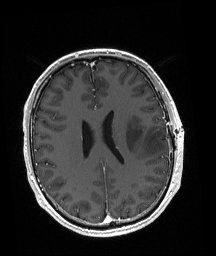
Brain MRI from a brain-tumour surgery series, one axial slice; position 77 of 192 along the scan axis; T1-weighted post-contrast; 1 mm slice thickness; 216 × 256 image matrix, field of view 211 × 250 mm. From the clinical record (not read from this slice): histopathology: Astrocytoma; WHO grade: 3; IDH mutation: yes; tumour location: Left Posterior Frontal.
Annotated regions visible in this slice (outlined manually by an expert reader):
- tumour: bounding box <125,124,167,155> (left, top, right, bottom; pixels)